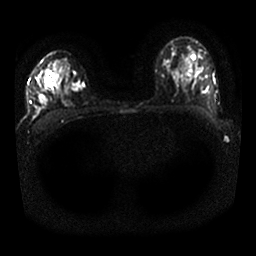
Breast MRI, one axial slice; slice 16 of 25 in the series (ordered by position); diffusion-weighted series; image 2 of 4 stored at this slice position (different b-values; order by instance number); 1.5 T; 256 × 256 image matrix, field of view 330 × 330 mm. Female patient.
Structures marked on this image (manually delineated by an expert):
- tumour on diffusion-weighted imaging: bounding box [x1, y1, x2, y2] px = [72, 83, 83, 92]